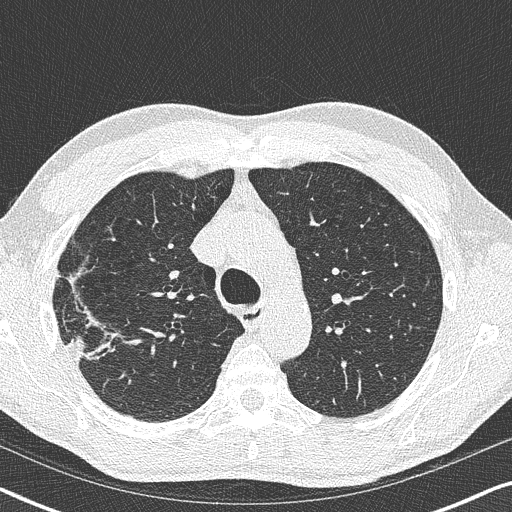
Low-dose screening chest CT, one axial slice. Position 268 of 356 along the scan axis. 120 kVp. Lung window (W 1500 / L -600 HU). 1 mm slice thickness. 512 × 512 image matrix, field of view 330 × 330 mm.
Outlined on this slice (manually delineated by an expert):
- lesion 1 (tumor, upper lobe of right lung): bounding box <66,334,89,368> (left, top, right, bottom; pixels)